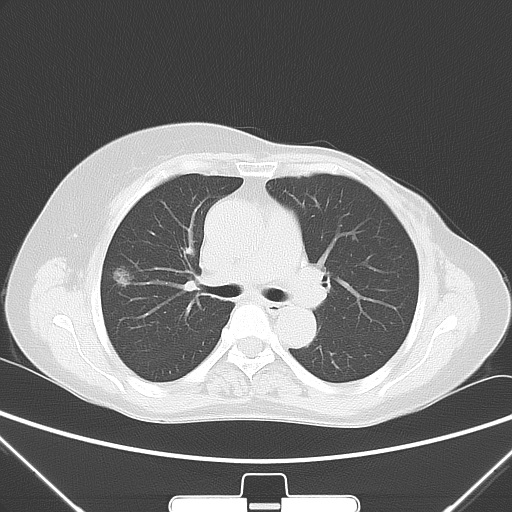
Chest CT, one axial slice. Position 32 of 53 along the scan axis. 120 kVp. Lung window (W 1500 / L -600 HU). 5 mm slice thickness. 512 × 512 image matrix, field of view 350 × 350 mm. Female patient, age 64 years. From the clinical record (not read from this slice): clinical TNM (as recorded): T1c N0 M0.
Structures marked on this image (bounding box drawn by a radiologist):
- lung tumour (recorded histology: adenocarcinoma): bounding box <107,259,136,288> (left, top, right, bottom; pixels)